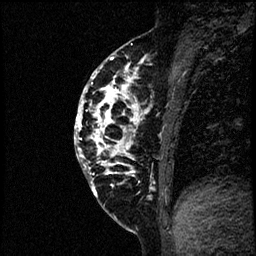
Breast MRI (dynamic contrast-enhanced), one sagittal slice; dynamic contrast-enhanced study with each time point stored as its own series, time point 2 of 4 at this slice position (early post-contrast, ordered by acquisition time); 1.5 T; TE 4.2 ms, TR 17.6 ms; 2 mm slice thickness; 256 × 256 image matrix, field of view 200 × 200 mm. Patient: female, 40 years. Case-level facts recorded for this patient, not image findings: setting: breast cancer imaged before/during neoadjuvant chemotherapy; receptor status: HER2-positive.
Outlined on this slice (semi-automatically segmented with operator editing):
- analysis volume of interest (the breast-tissue region the enhancement analysis was run in; not a lesion): bounding box <75,56,197,205> (left, top, right, bottom; pixels)
- tumour enhancement mask (voxels above the 100 % enhancement threshold inside the analysis volume of interest): <75,57,152,197>